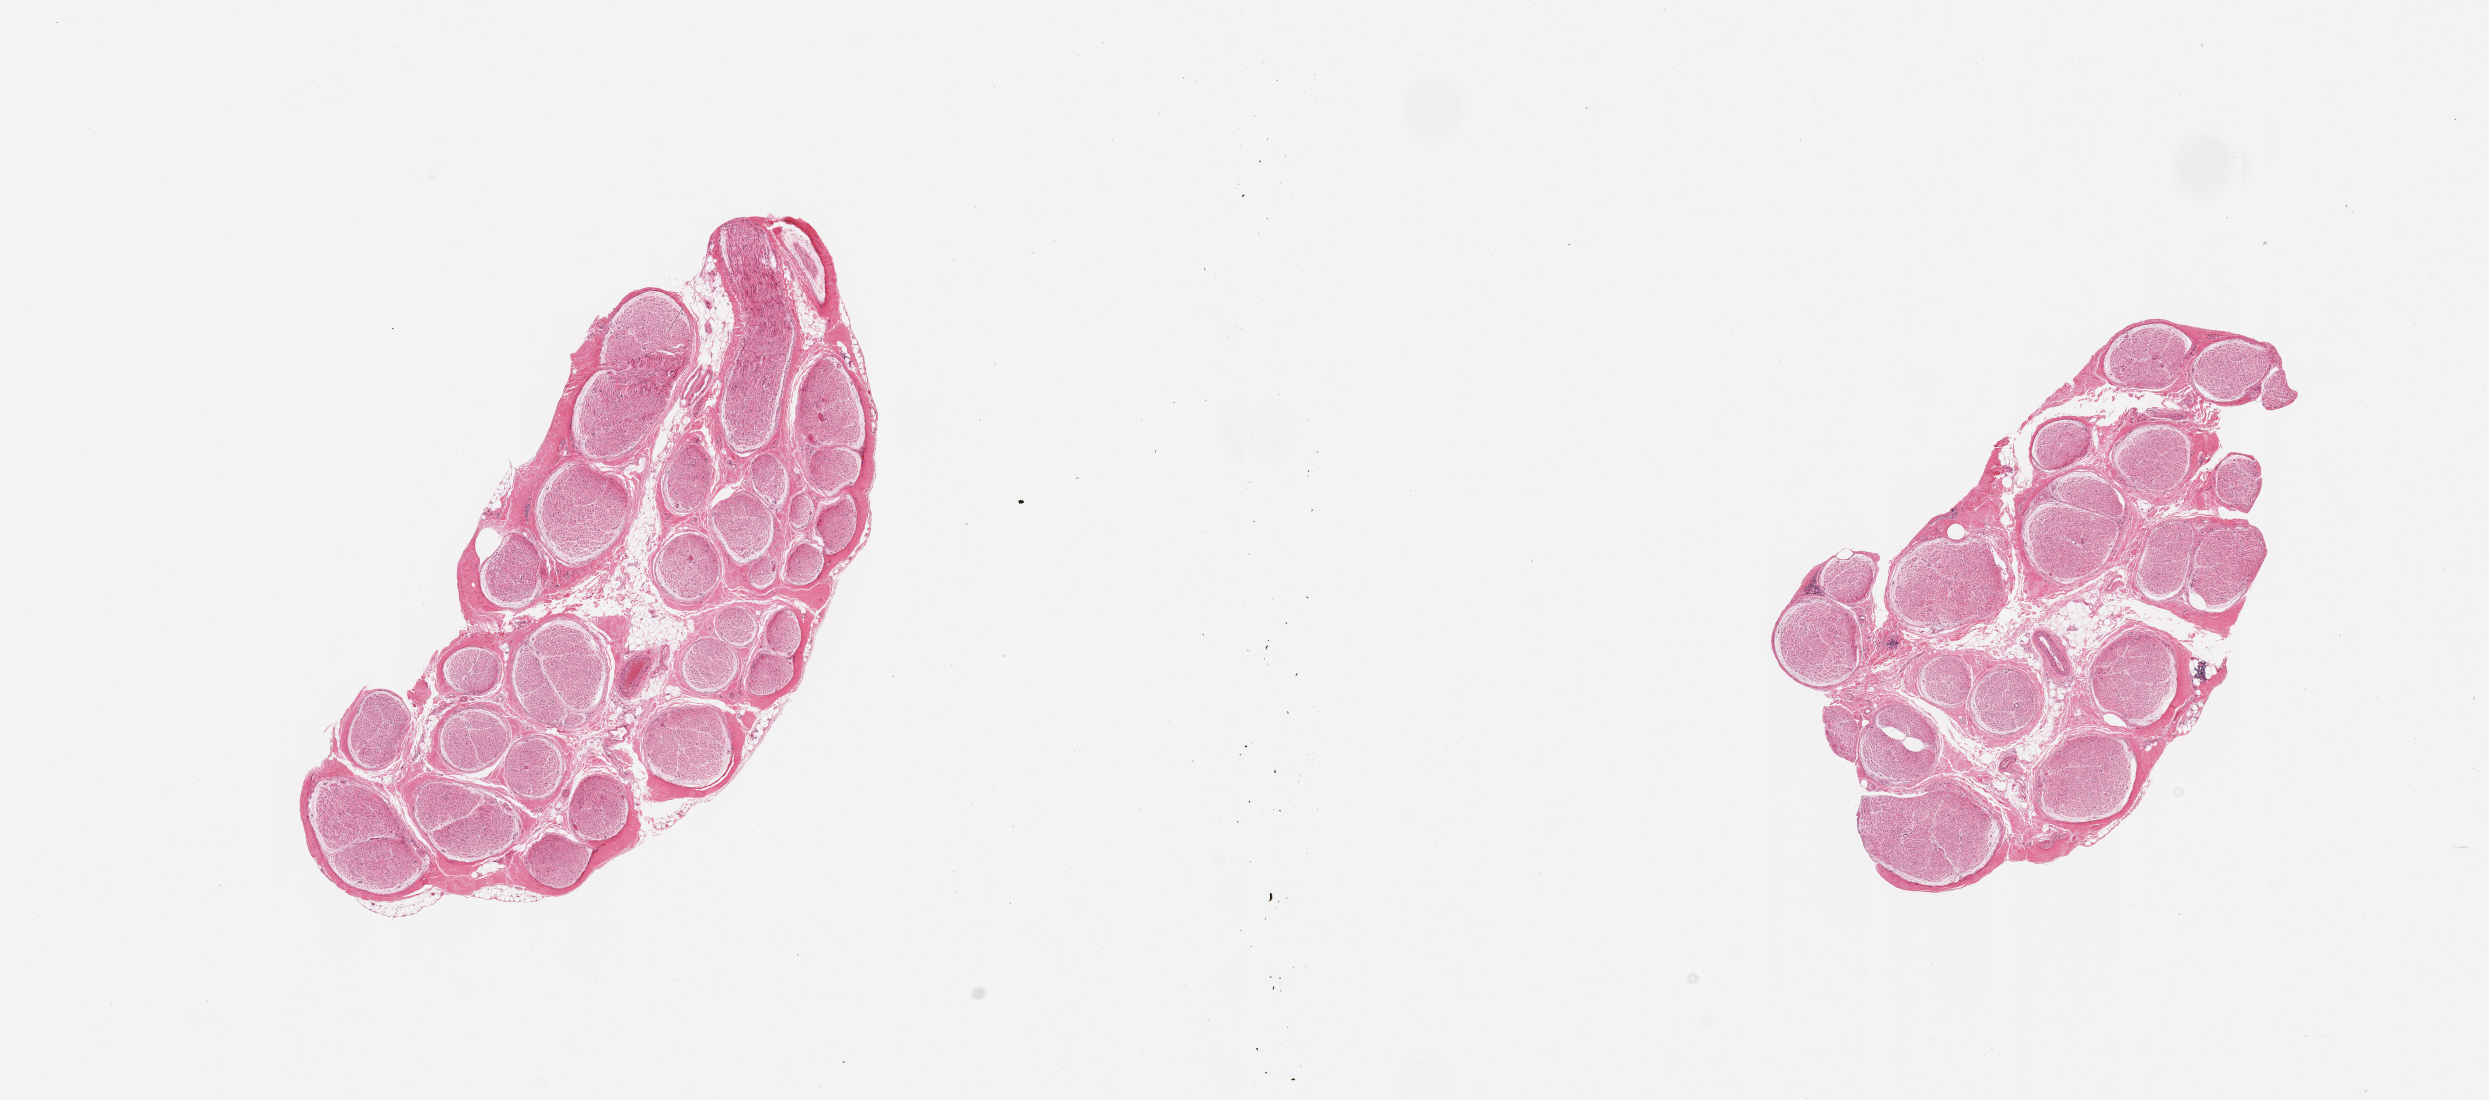
Digitized H&E-stained section, a low-resolution overview of the entire scanned area, about 19.7 x 8.7 mm (from a 20x scan). PAXgene-fixed, paraffin-embedded tissue. Target tissue: tibial nerve. Donor tissue sample.
• reviewer comment on this tissue sample: 2 pieces; ~5% internal fat and trace of external fat; mild focal lymphocytic infiltrate in perineural tissue